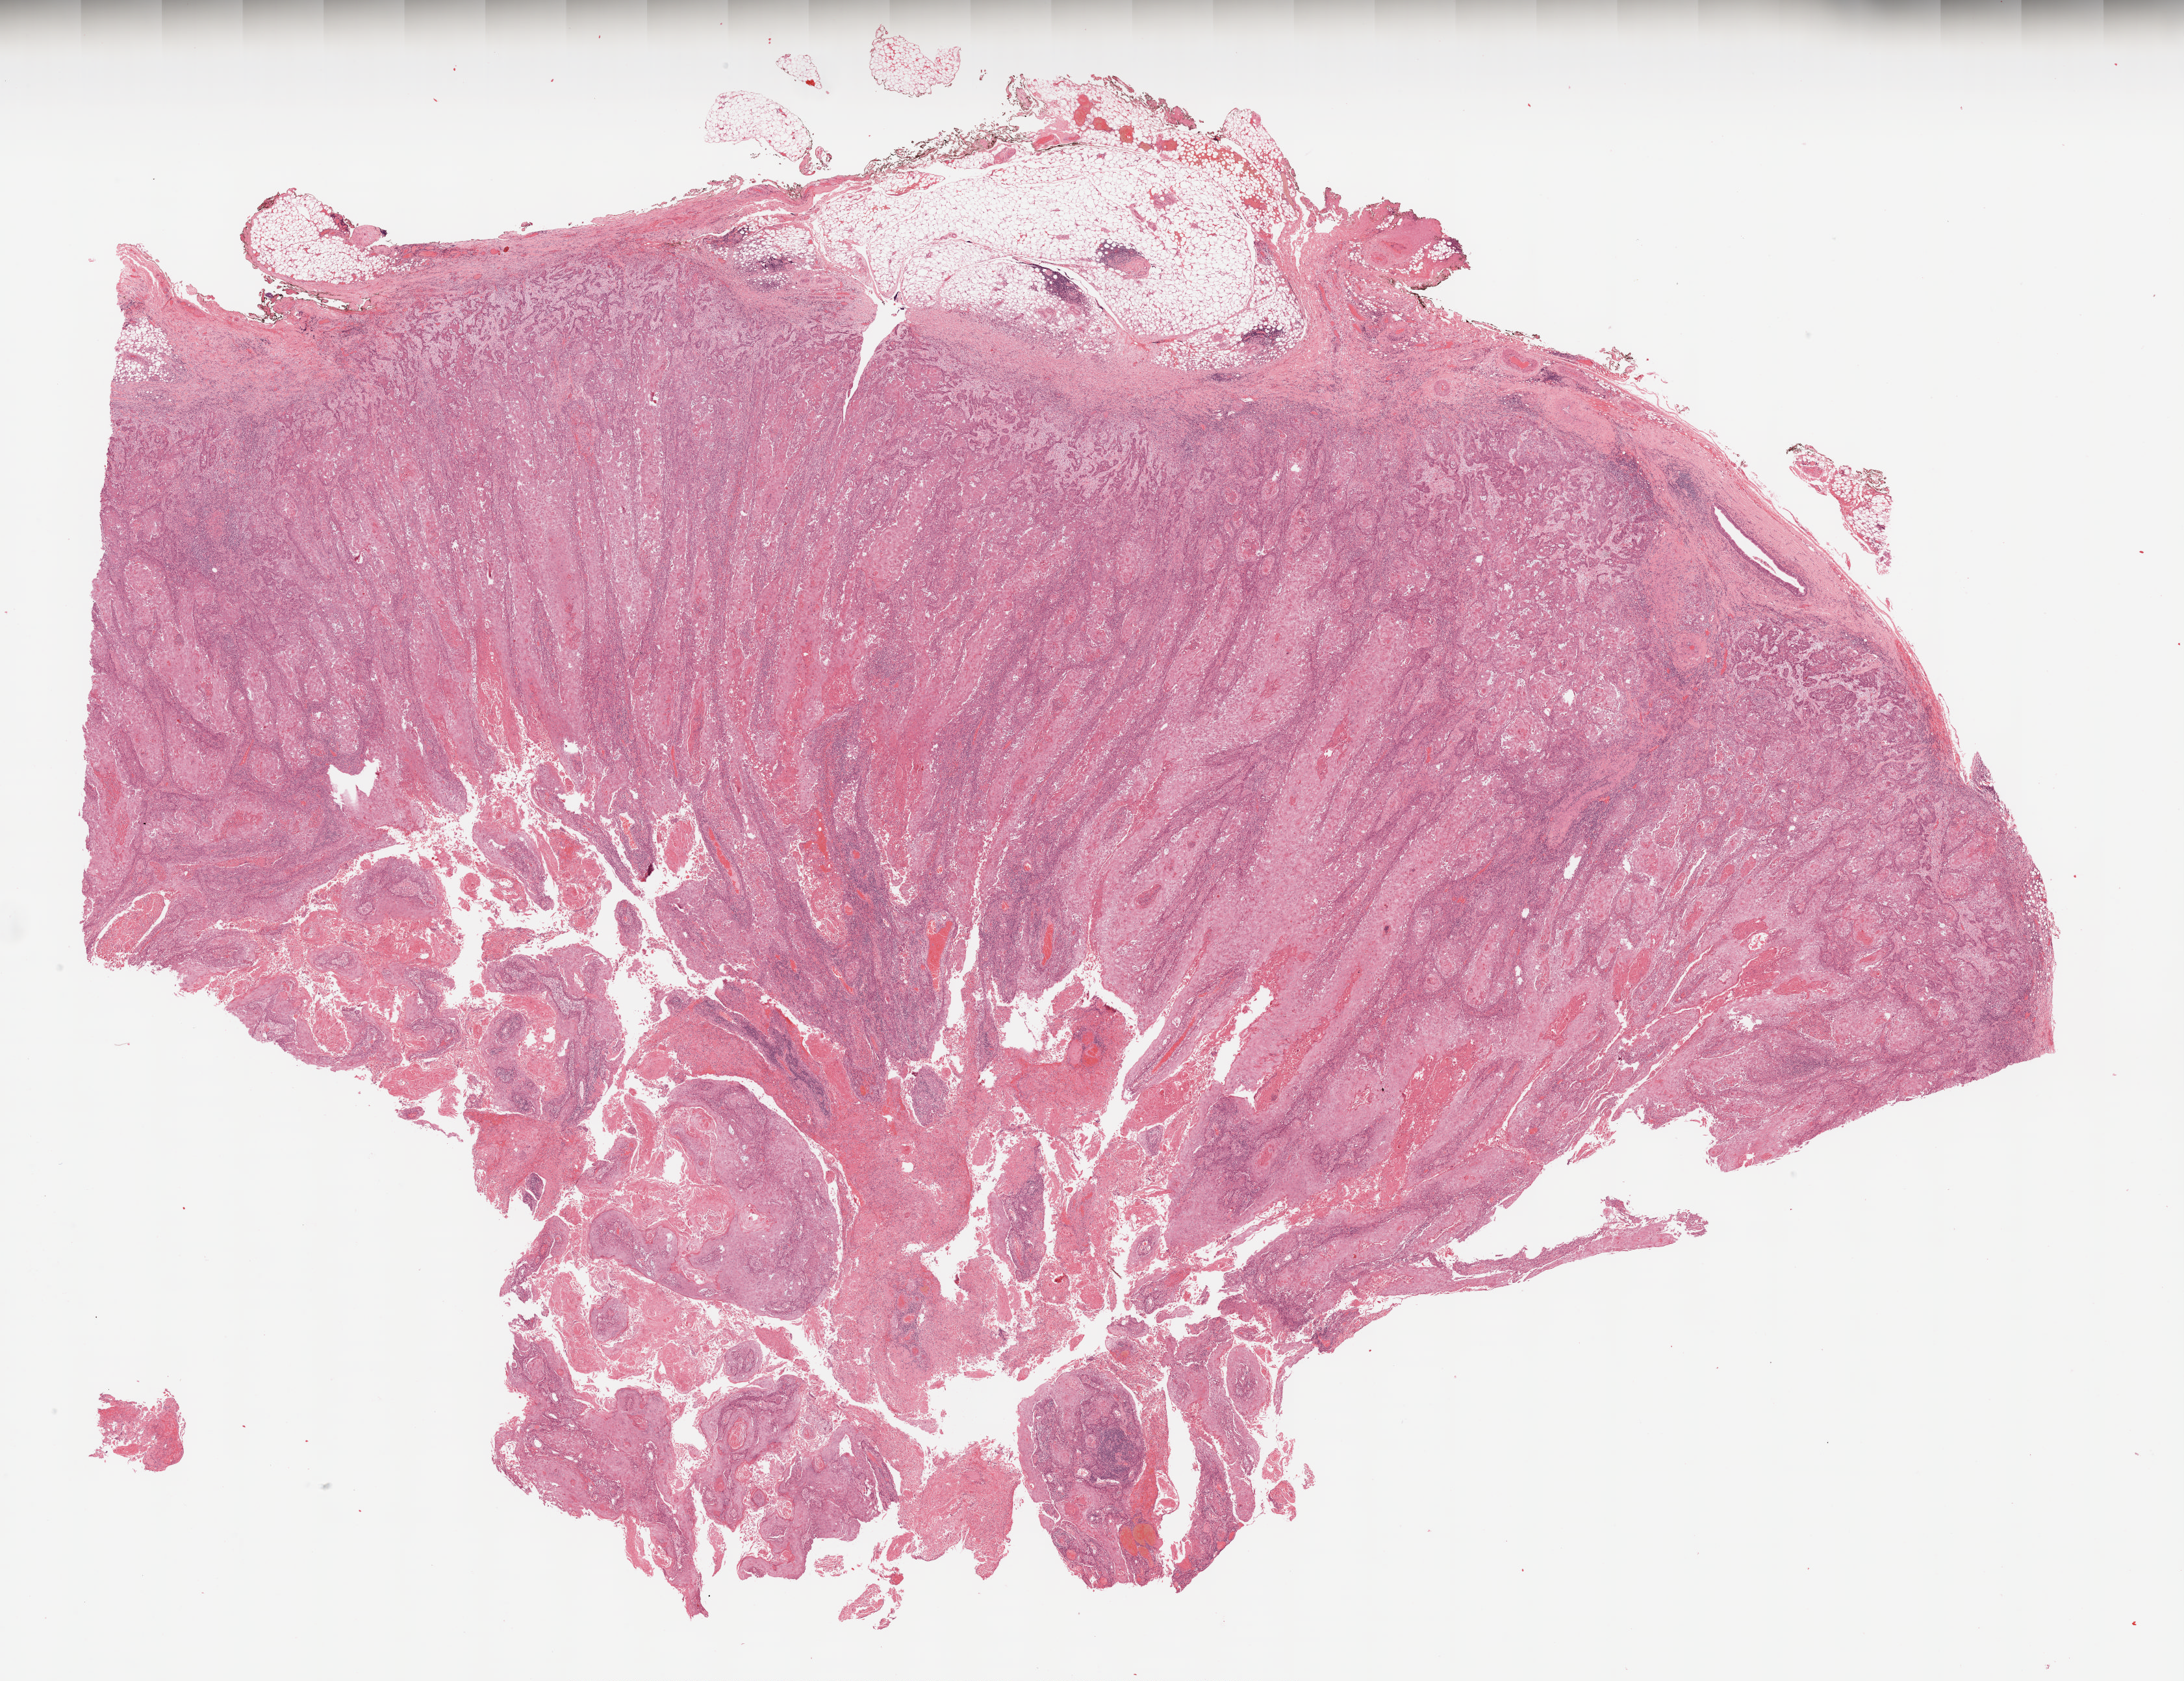
Whole-slide histology image, H&E — whole scanned area (about 27.0 x 20.8 mm, acquisition: 20x scan) shown as a low-resolution overview. Formalin-fixed paraffin-embedded (FFPE) diagnostic section. Sample: primary tumour, head and neck. Patient: female, age at initial diagnosis 83 years. Histologic grade: G2 (moderately differentiated).
* histologic diagnosis: Squamous cell carcinoma, NOS
* AJCC pathologic stage: III (6th edition)